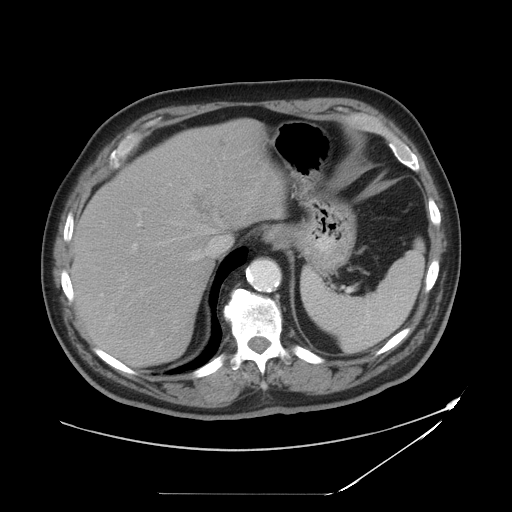
Contrast-enhanced abdominal CT, one axial slice. Position 35 of 49 along the scan axis. Reconstruction kernel STANDARD. 120 kVp. Soft-tissue window (W 400 / L 40 HU). 5 mm slice thickness. 512 × 512 image matrix, field of view 461 × 461 mm. Male patient, age 72 years. From the clinical record (not read from this slice): diagnosis: colorectal cancer liver metastases, imaged before liver resection; multiple liver metastases: no; largest metastasis: 2.5 cm; disease in both lobes: no.
Structures marked on this image (expert manual segmentation):
- hepatic veins: bounding box (x1, y1, x2, y2) in pixels: (122, 223, 222, 288)
- liver: (75, 121, 282, 365)
- planned liver remnant (the part of the liver to remain after resection): (75, 177, 212, 365)
- portal vein (with intrahepatic branches): (133, 152, 244, 295)
- liver metastasis: (194, 195, 213, 216)